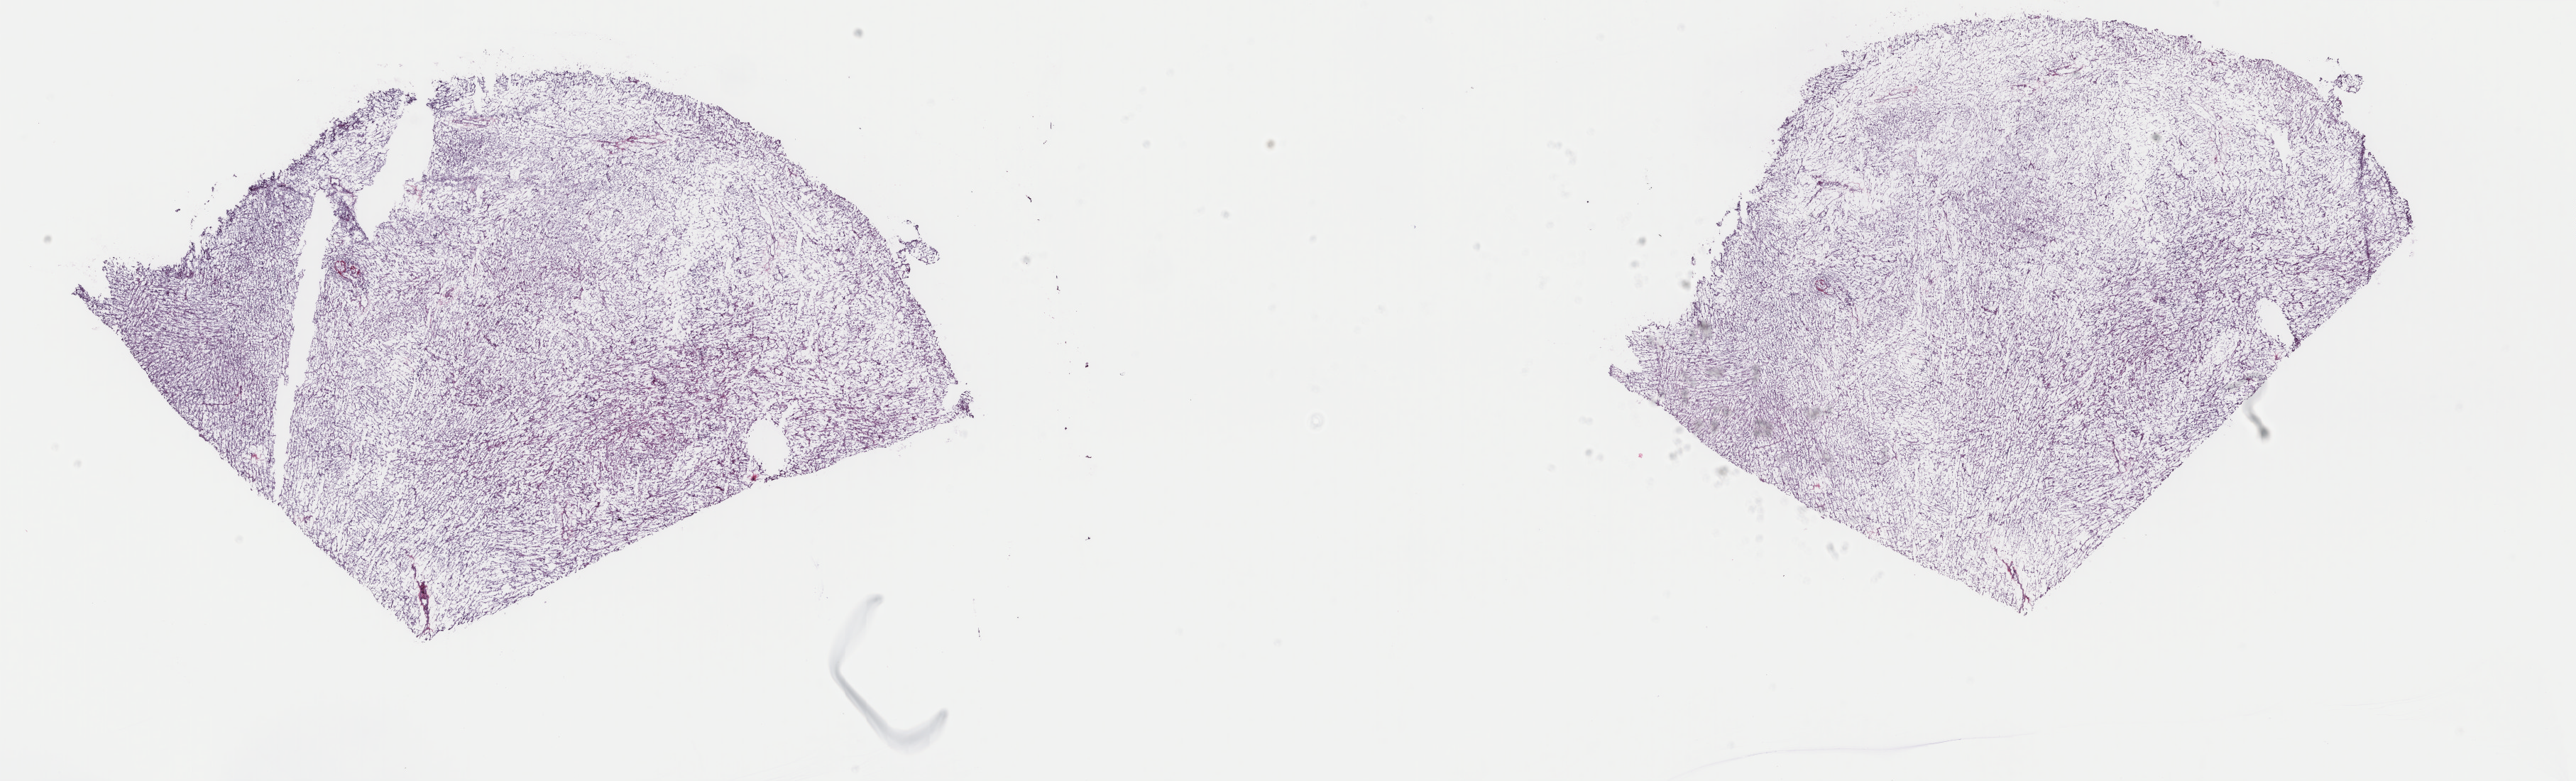
H&E-stained whole-slide image — a low-resolution overview of the entire scanned area, about 28.8 x 8.7 mm; frozen section from the top of the tissue portion; primary tumour sample from the connective, subcutaneous and other soft tissues. Male patient; age at initial diagnosis 42 years. Pathologist review of this section (percent, as recorded): tumour cells 100%, tumour nuclei 80%, normal cells 0%, stromal cells 0%, necrosis 0%. Infiltration values recorded for this section: lymphocyte infiltration 0%, monocyte infiltration 0%, neutrophil infiltration 0%.
* pathologic diagnosis: Leiomyosarcoma, NOS (connective, subcutaneous and other soft tissues of pelvis)